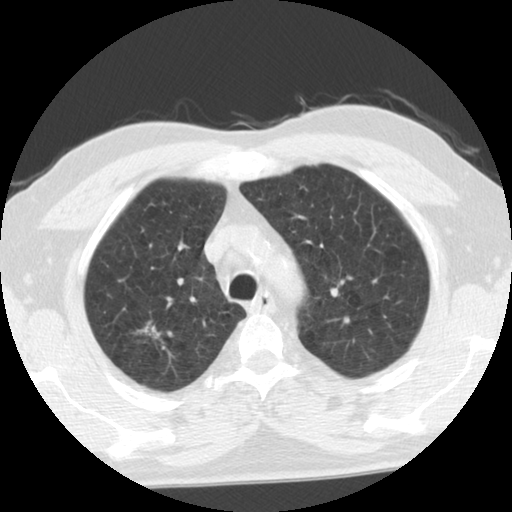
Low-dose screening chest CT, axial slice, second annual screen, lung window (W 1500 / L -600 HU), standard (soft-tissue) reconstruction kernel (STANDARD), 140 kVp. Male, age 68 years at enrolment. Former smoker at enrolment.
Lesion marked by an expert reader, bounding box <130,312,171,348> (left, top, right, bottom; pixels). The exam's reader record, not a measurement of the box and not confirmed to be the same lesion: non-calcified nodule or mass ≥4 mm, right upper lobe, poorly defined margins, ground glass attenuation, pre-existing on the prior screen: yes; interval growth: yes. Lung cancer was diagnosed 88 days after this screen: adenocarcinoma, NOS, right upper lobe, moderately differentiated (G2), stage IA (AJCC 6th edition), 28 mm at pathology.